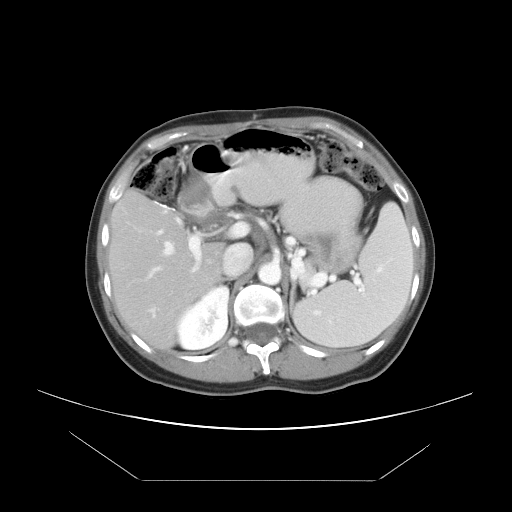
Contrast-enhanced abdominal CT, one axial slice. Slice 28 of 45 in the series (ordered by position). Reconstruction kernel STANDARD. 120 kVp. Intravenous contrast given. Soft-tissue window (W 400 / L 40 HU). 5 mm slice thickness. 512 × 512 image matrix, field of view 405 × 405 mm. Female patient, age 52 years. From the clinical record (not read from this slice): diagnosis: colorectal cancer liver metastases, imaged before liver resection; multiple liver metastases: yes; largest metastasis: 2.5 cm.
Annotated regions visible in this slice (manually delineated by an expert):
- hepatic veins: bounding box <151,242,173,311> (left, top, right, bottom; pixels)
- liver: <112,195,224,345>
- planned liver remnant (the part of the liver to remain after resection): <112,195,224,344>
- portal vein (with intrahepatic branches): <156,218,233,273>